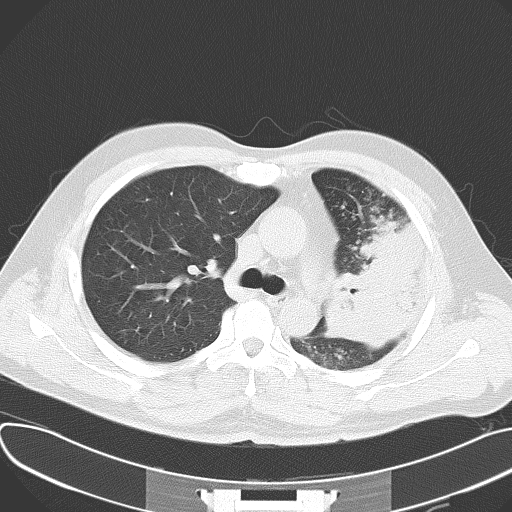
Chest CT, one axial slice; slice 42 of 62 in the series (ordered by position); lung window (W 1500 / L -600 HU); 512 × 512 image matrix, field of view 377 × 377 mm. Patient: male, 48 years. Case-level facts recorded for this patient, not image findings: clinical TNM (as recorded): T4 N0 M0.
Structures marked on this image (rectangle marked by the reading radiologist):
- lung tumour (recorded histology: adenocarcinoma): bounding box (x1, y1, x2, y2) in pixels: (329, 218, 425, 350)